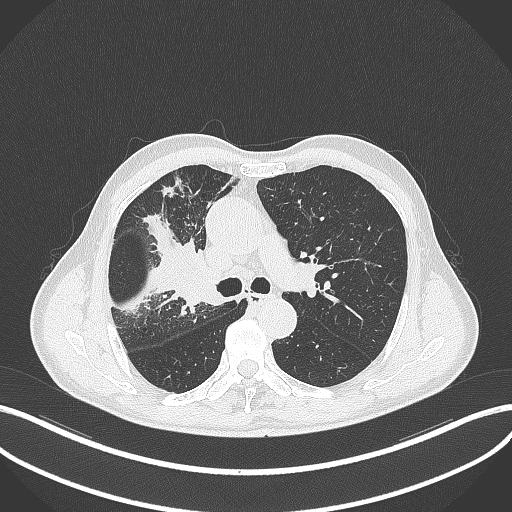
Chest CT, one axial slice; slice 316 of 490 in the series (ordered by position); reconstruction kernel B70f; 120 kVp; lung window (W 1500 / L -600 HU); 1 mm slice thickness; 512 × 512 image matrix. Patient: male, 69 years. From the clinical record (not read from this slice): clinical TNM (as recorded): T2a N0 M0.
Outlined on this slice (bounding box drawn by a radiologist):
- lung tumour (recorded histology: adenocarcinoma): box from (x=162, y=237) to (x=226, y=314) px